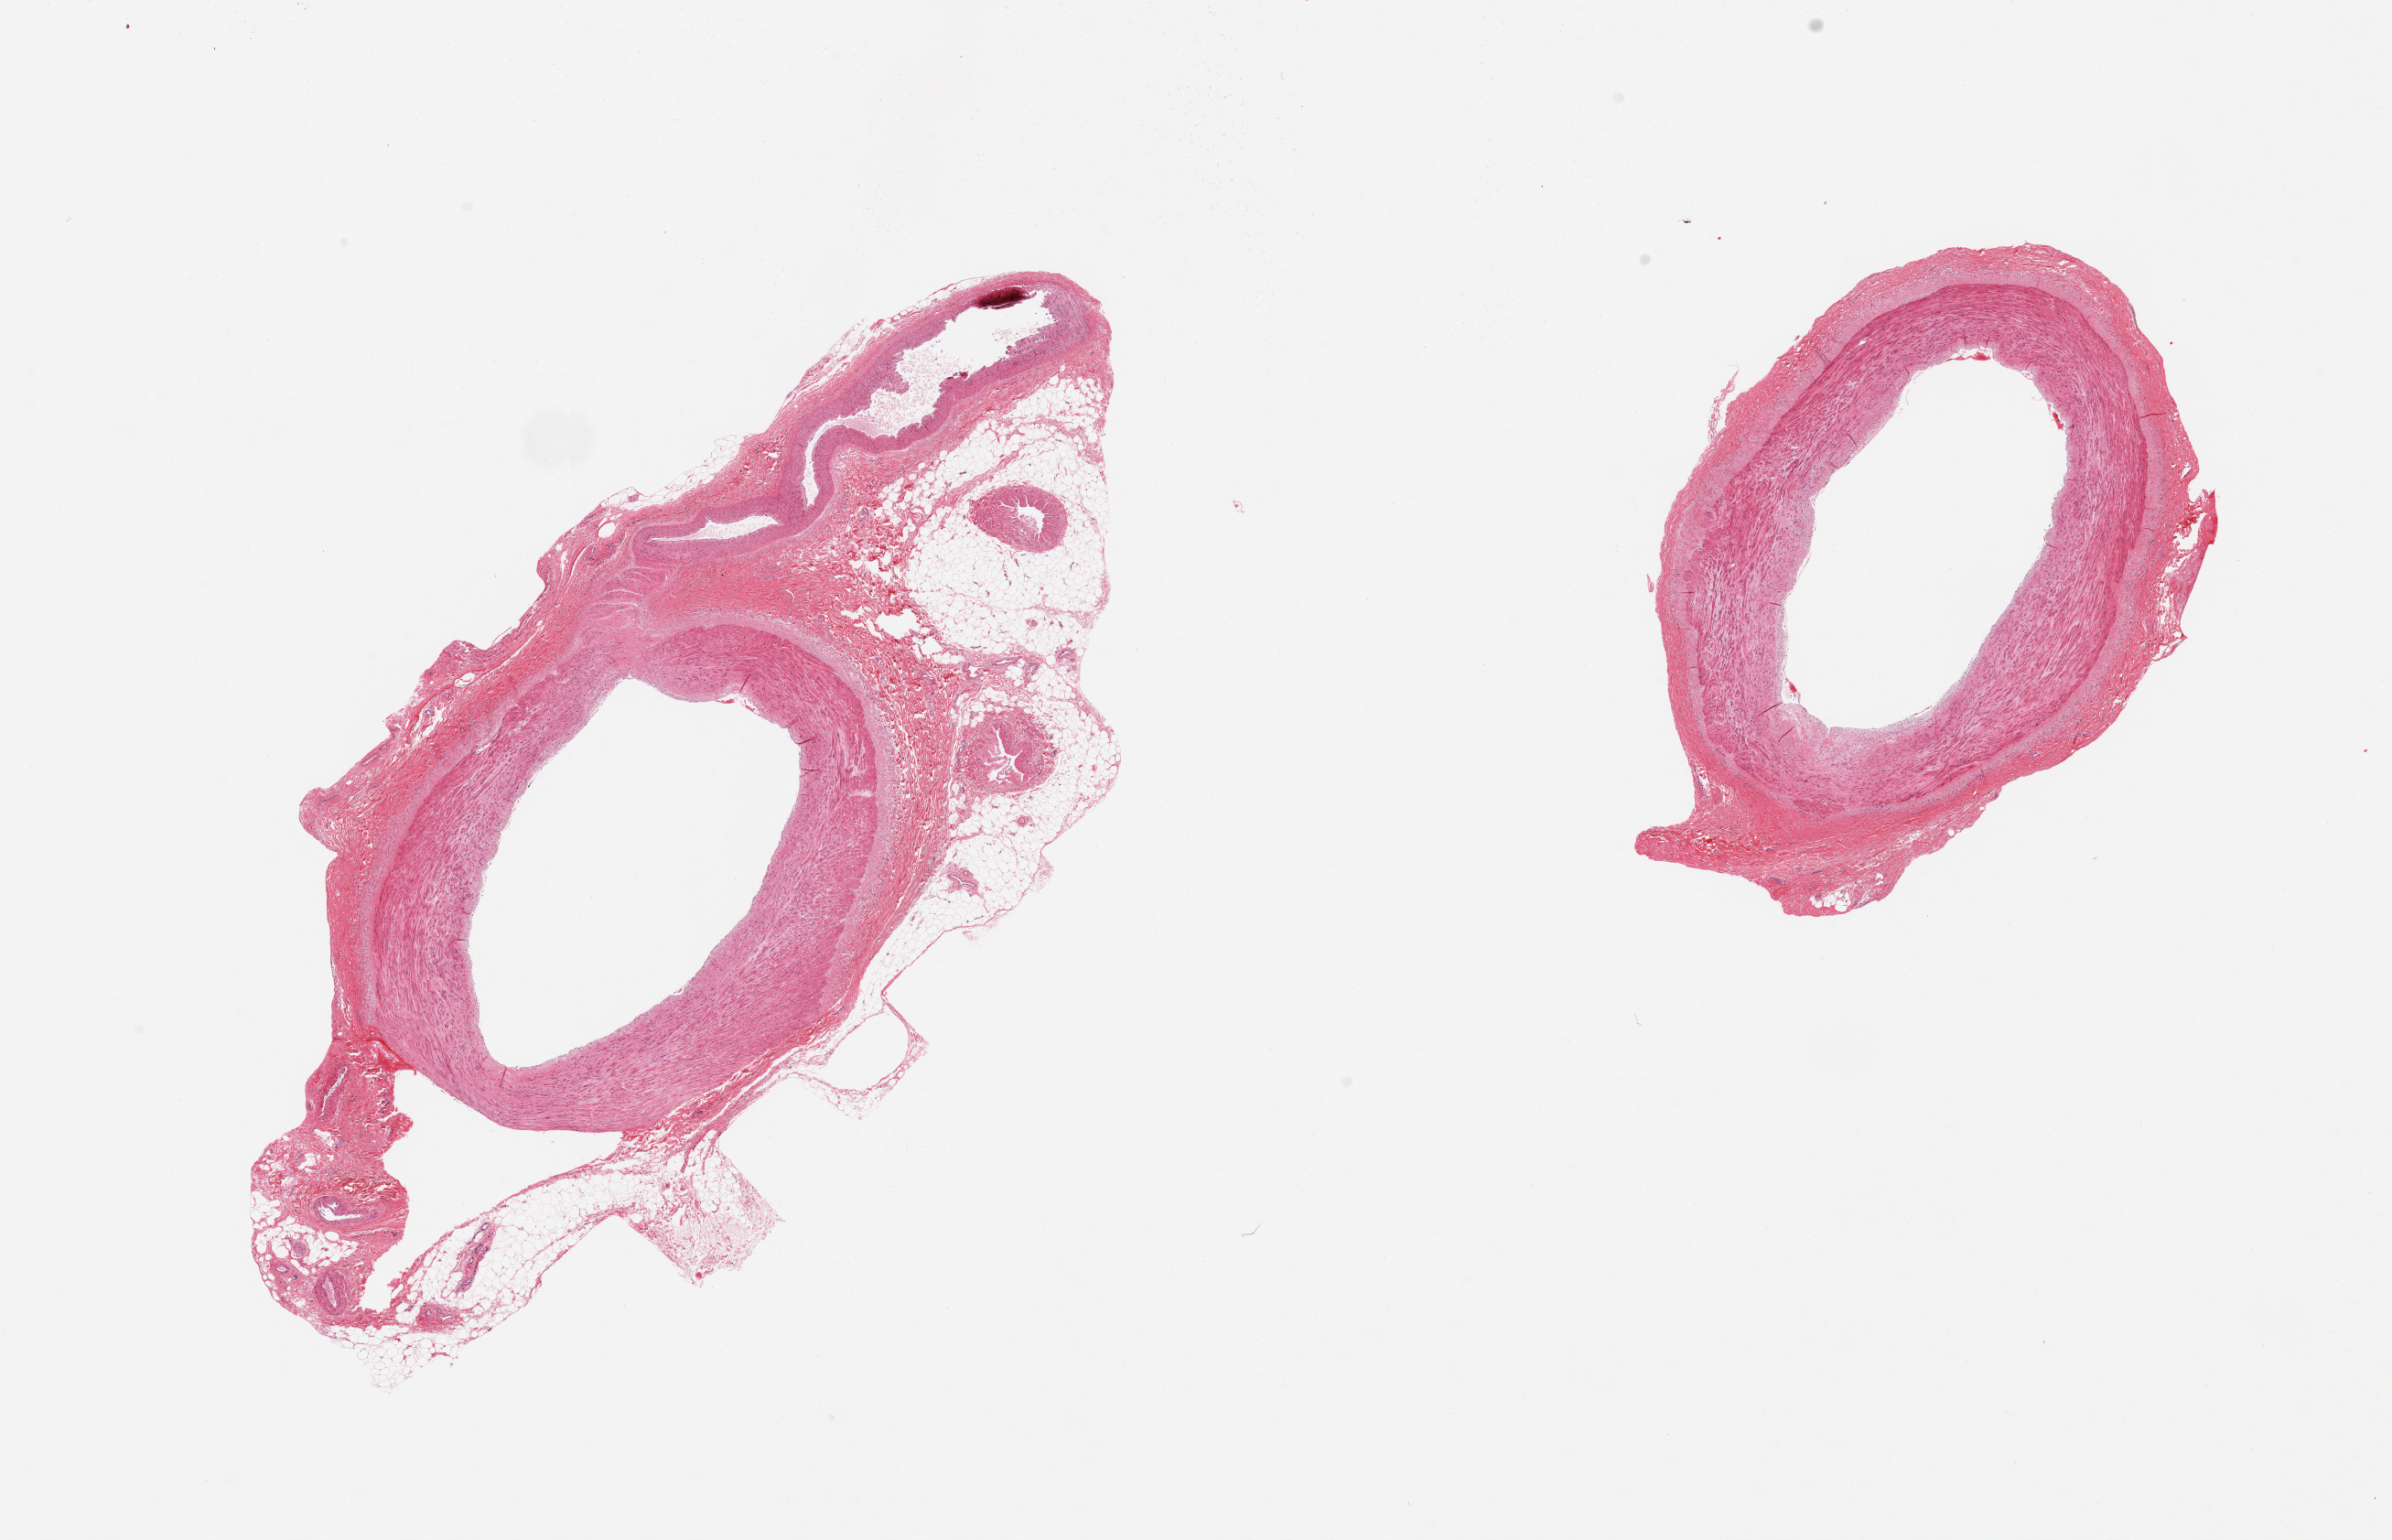
Whole-slide image, haematoxylin and eosin stain — low-resolution overview of the scanned area, about 20.7 x 13.3 mm (slide scanned at 20x); PAXgene-fixed paraffin-embedded (PFPE) section; target tissue: tibial artery; donor tissue sample. Donor: female.
Pathologist's review note for this sample: 2 pieces; 20% external fat on 1 piece.